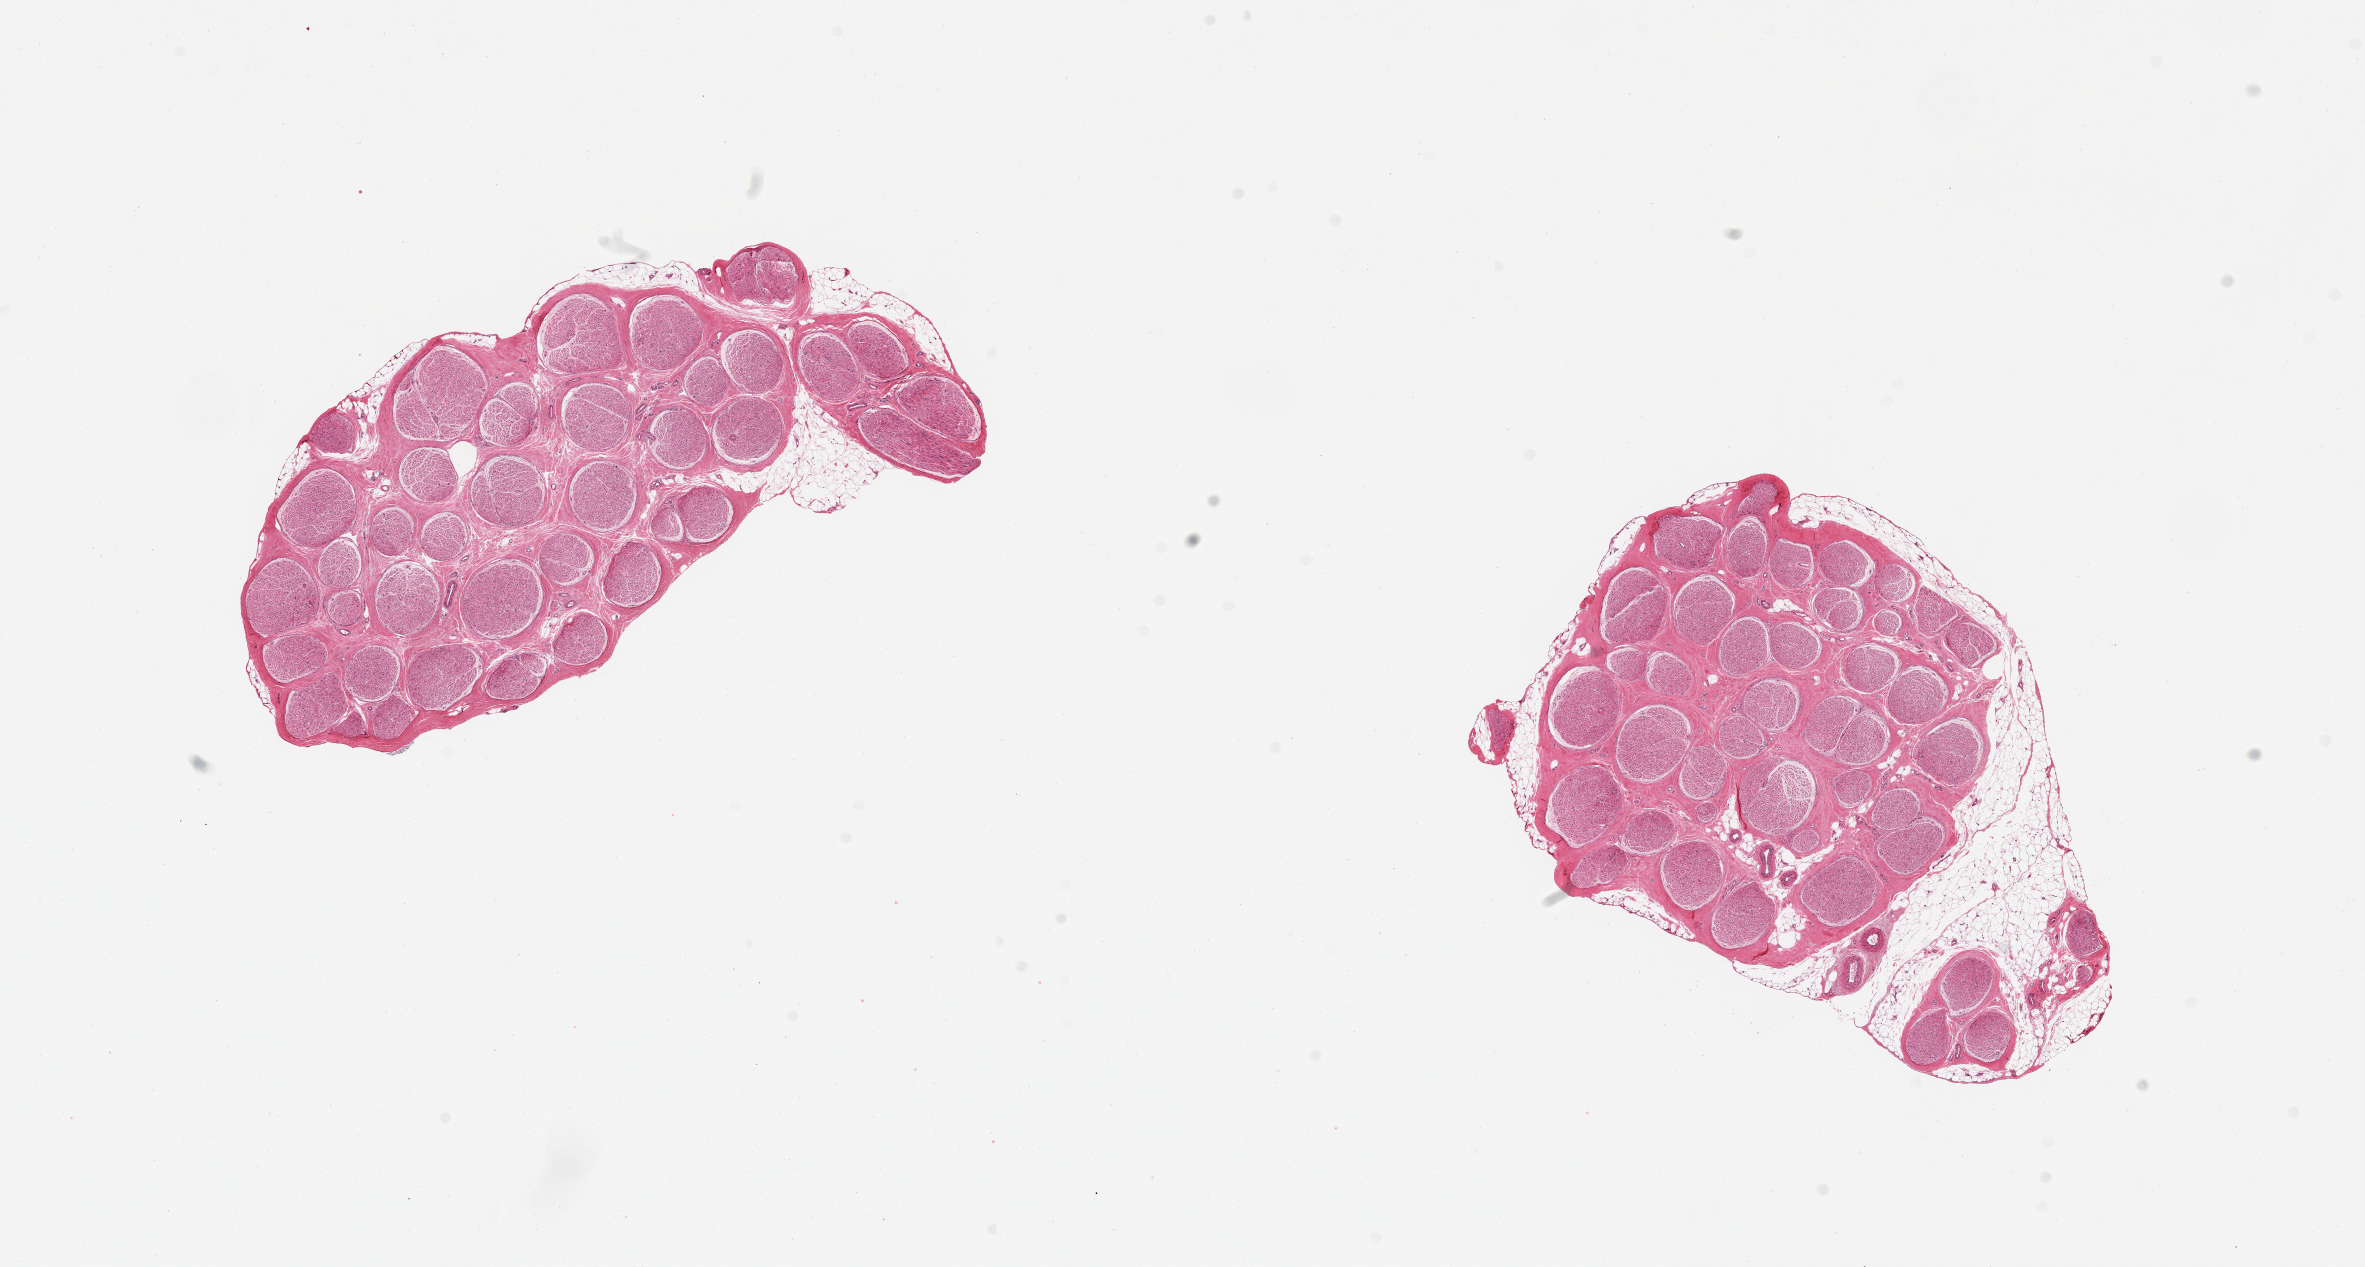
Digitized H&E-stained section — whole scanned area (about 18.7 x 10.0 mm, acquisition: 20x scan) shown as a low-resolution overview, PAXgene-fixed paraffin-embedded (PFPE) section, target tissue: tibial nerve, donor tissue sample. Donor sex: female.
• pathologist's review note for this sample: 2 pieces, generally clean rim of adherent fat <0.1mm, small 1mm aggregate of interstitial fat